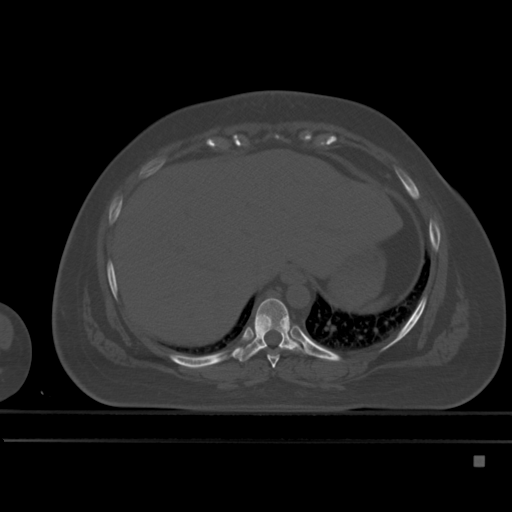
CT including the spine, one axial slice; position 267 of 495 along the scan axis; bone window (W 1800 / L 400 HU); 1.5 mm slice thickness; 512 × 512 image matrix, field of view 404 × 404 mm. Female patient, age 33 years. From the clinical record (not read from this slice): primary cancer: breast.
Outlined on this slice (semi-automatically segmented with operator editing):
- T8 vertebra: bounding box <267,355,279,368> (left, top, right, bottom; pixels)
- T9 vertebra: <231,297,310,362>